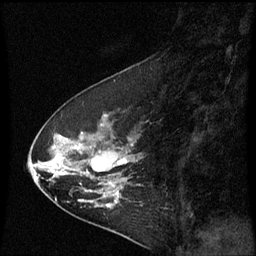
Breast MRI (dynamic contrast-enhanced), one sagittal slice. Position 23 of 60 along the scan axis. Dynamic contrast-enhanced series, image 2 of 3 at this slice position (ordered by acquisition). 1.5 T. TE 4.2 ms, TR 8.9 ms. 2 mm slice thickness. 256 × 256 image matrix. Patient: female, 53 years. From the clinical record (not read from this slice): setting: breast cancer imaged before/during neoadjuvant chemotherapy; receptor status: HR-positive, HER2-negative.
Structures marked on this image (semi-automatic segmentation, software-assisted and operator-edited):
- analysis volume of interest (the breast-tissue region the enhancement analysis was run in; not a lesion): box from (x=32, y=100) to (x=143, y=221) px
- tumour enhancement mask (voxels above the 70 % enhancement threshold inside the analysis volume of interest): (x=52, y=136)–(x=135, y=207)